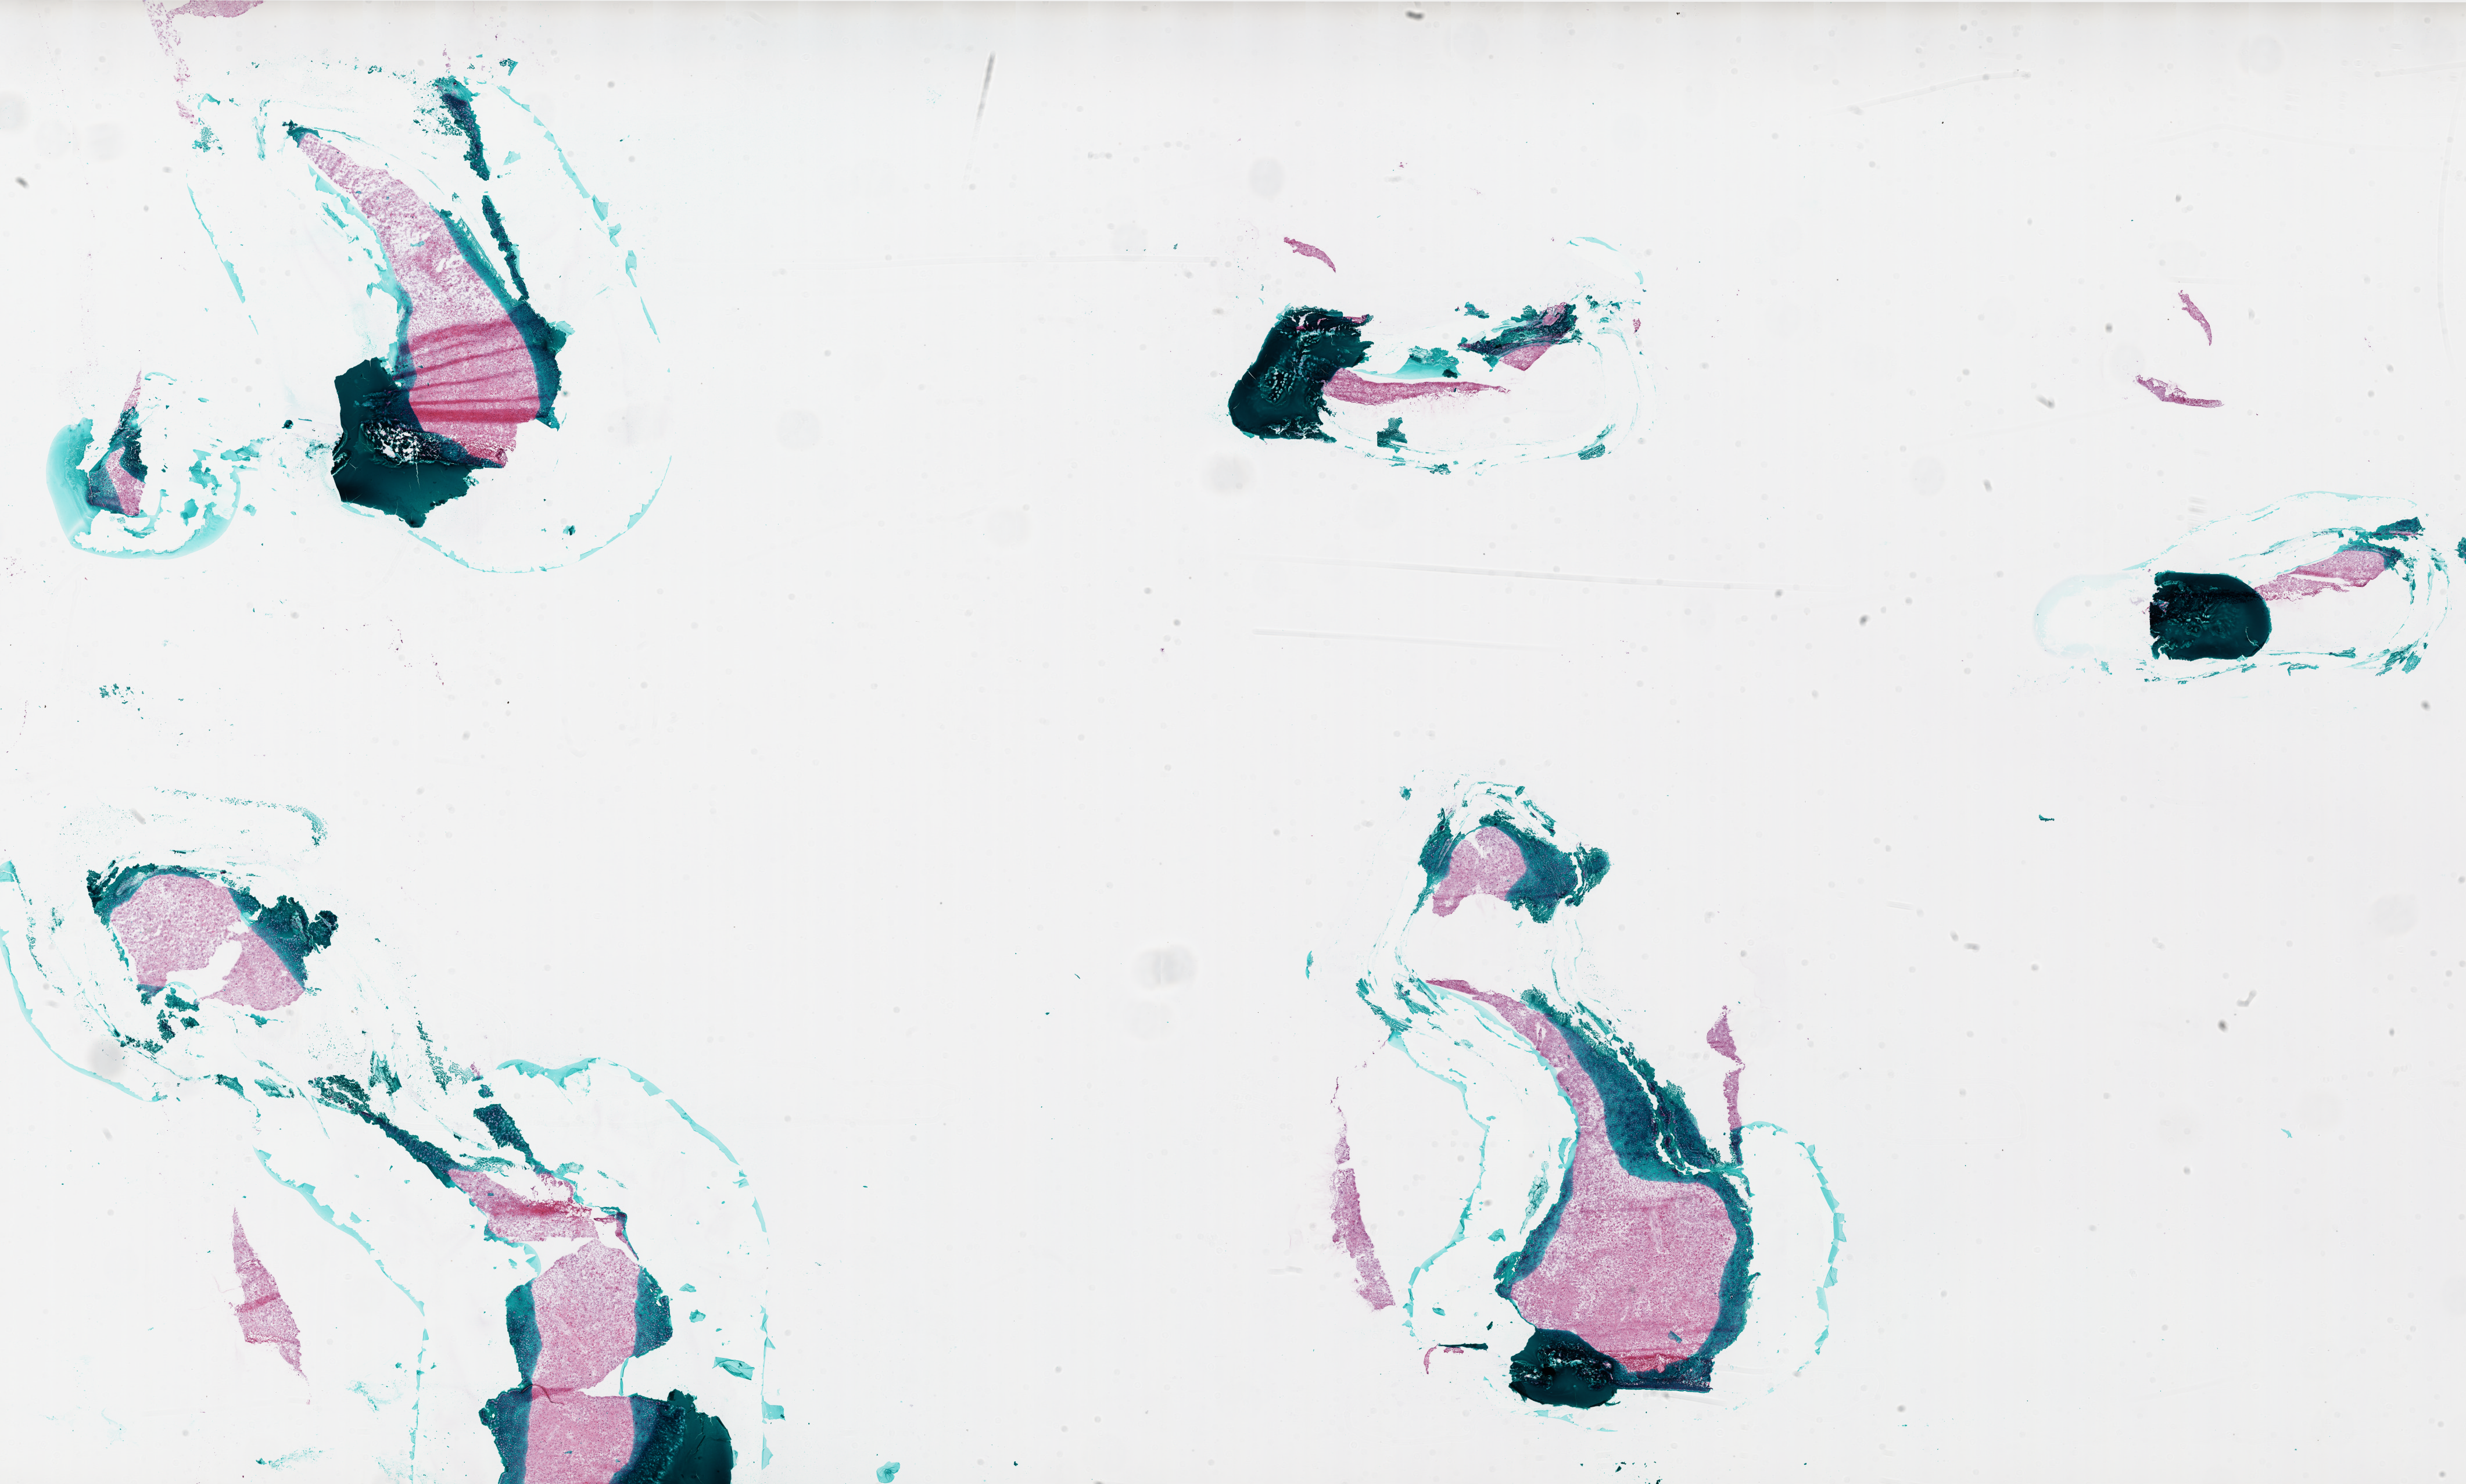
Hematoxylin and eosin (H&E) stained whole-slide image, shown as a low-resolution overview of the whole scanned area (about 34.0 x 20.4 mm, from a 20x scan). Frozen section from the bottom of the tissue portion. Primary tumour sample from the brain. Male patient; age at initial diagnosis 54 years. Slide review estimates, as recorded: tumour cells 95%, tumour nuclei 100%, normal cells 0%, stromal cells 0%, necrosis 5%.
Diagnosis: Glioblastoma.